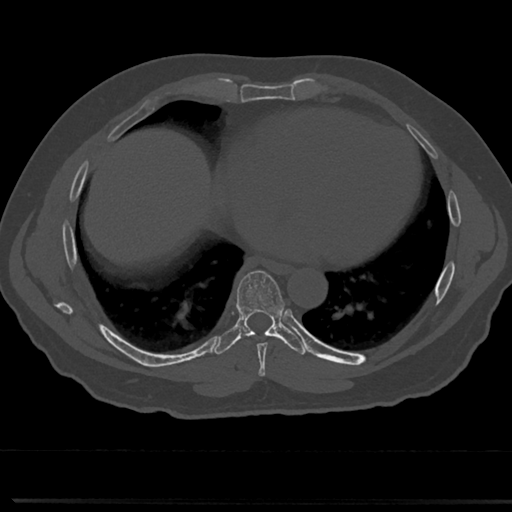
CT including the spine, one axial slice; slice 368 of 817 in the series (ordered by position); reconstruction kernel Br40s/3; bone window (W 1800 / L 400 HU); 512 × 512 image matrix, field of view 355 × 355 mm. Male patient, age 61 years. From the clinical record (not read from this slice): primary cancer: prostate.
Outlined on this slice (semi-automatically segmented with operator editing):
- T7 vertebra: bounding box <236,272,287,358> (left, top, right, bottom; pixels)
- T8 vertebra: <237,323,283,335>